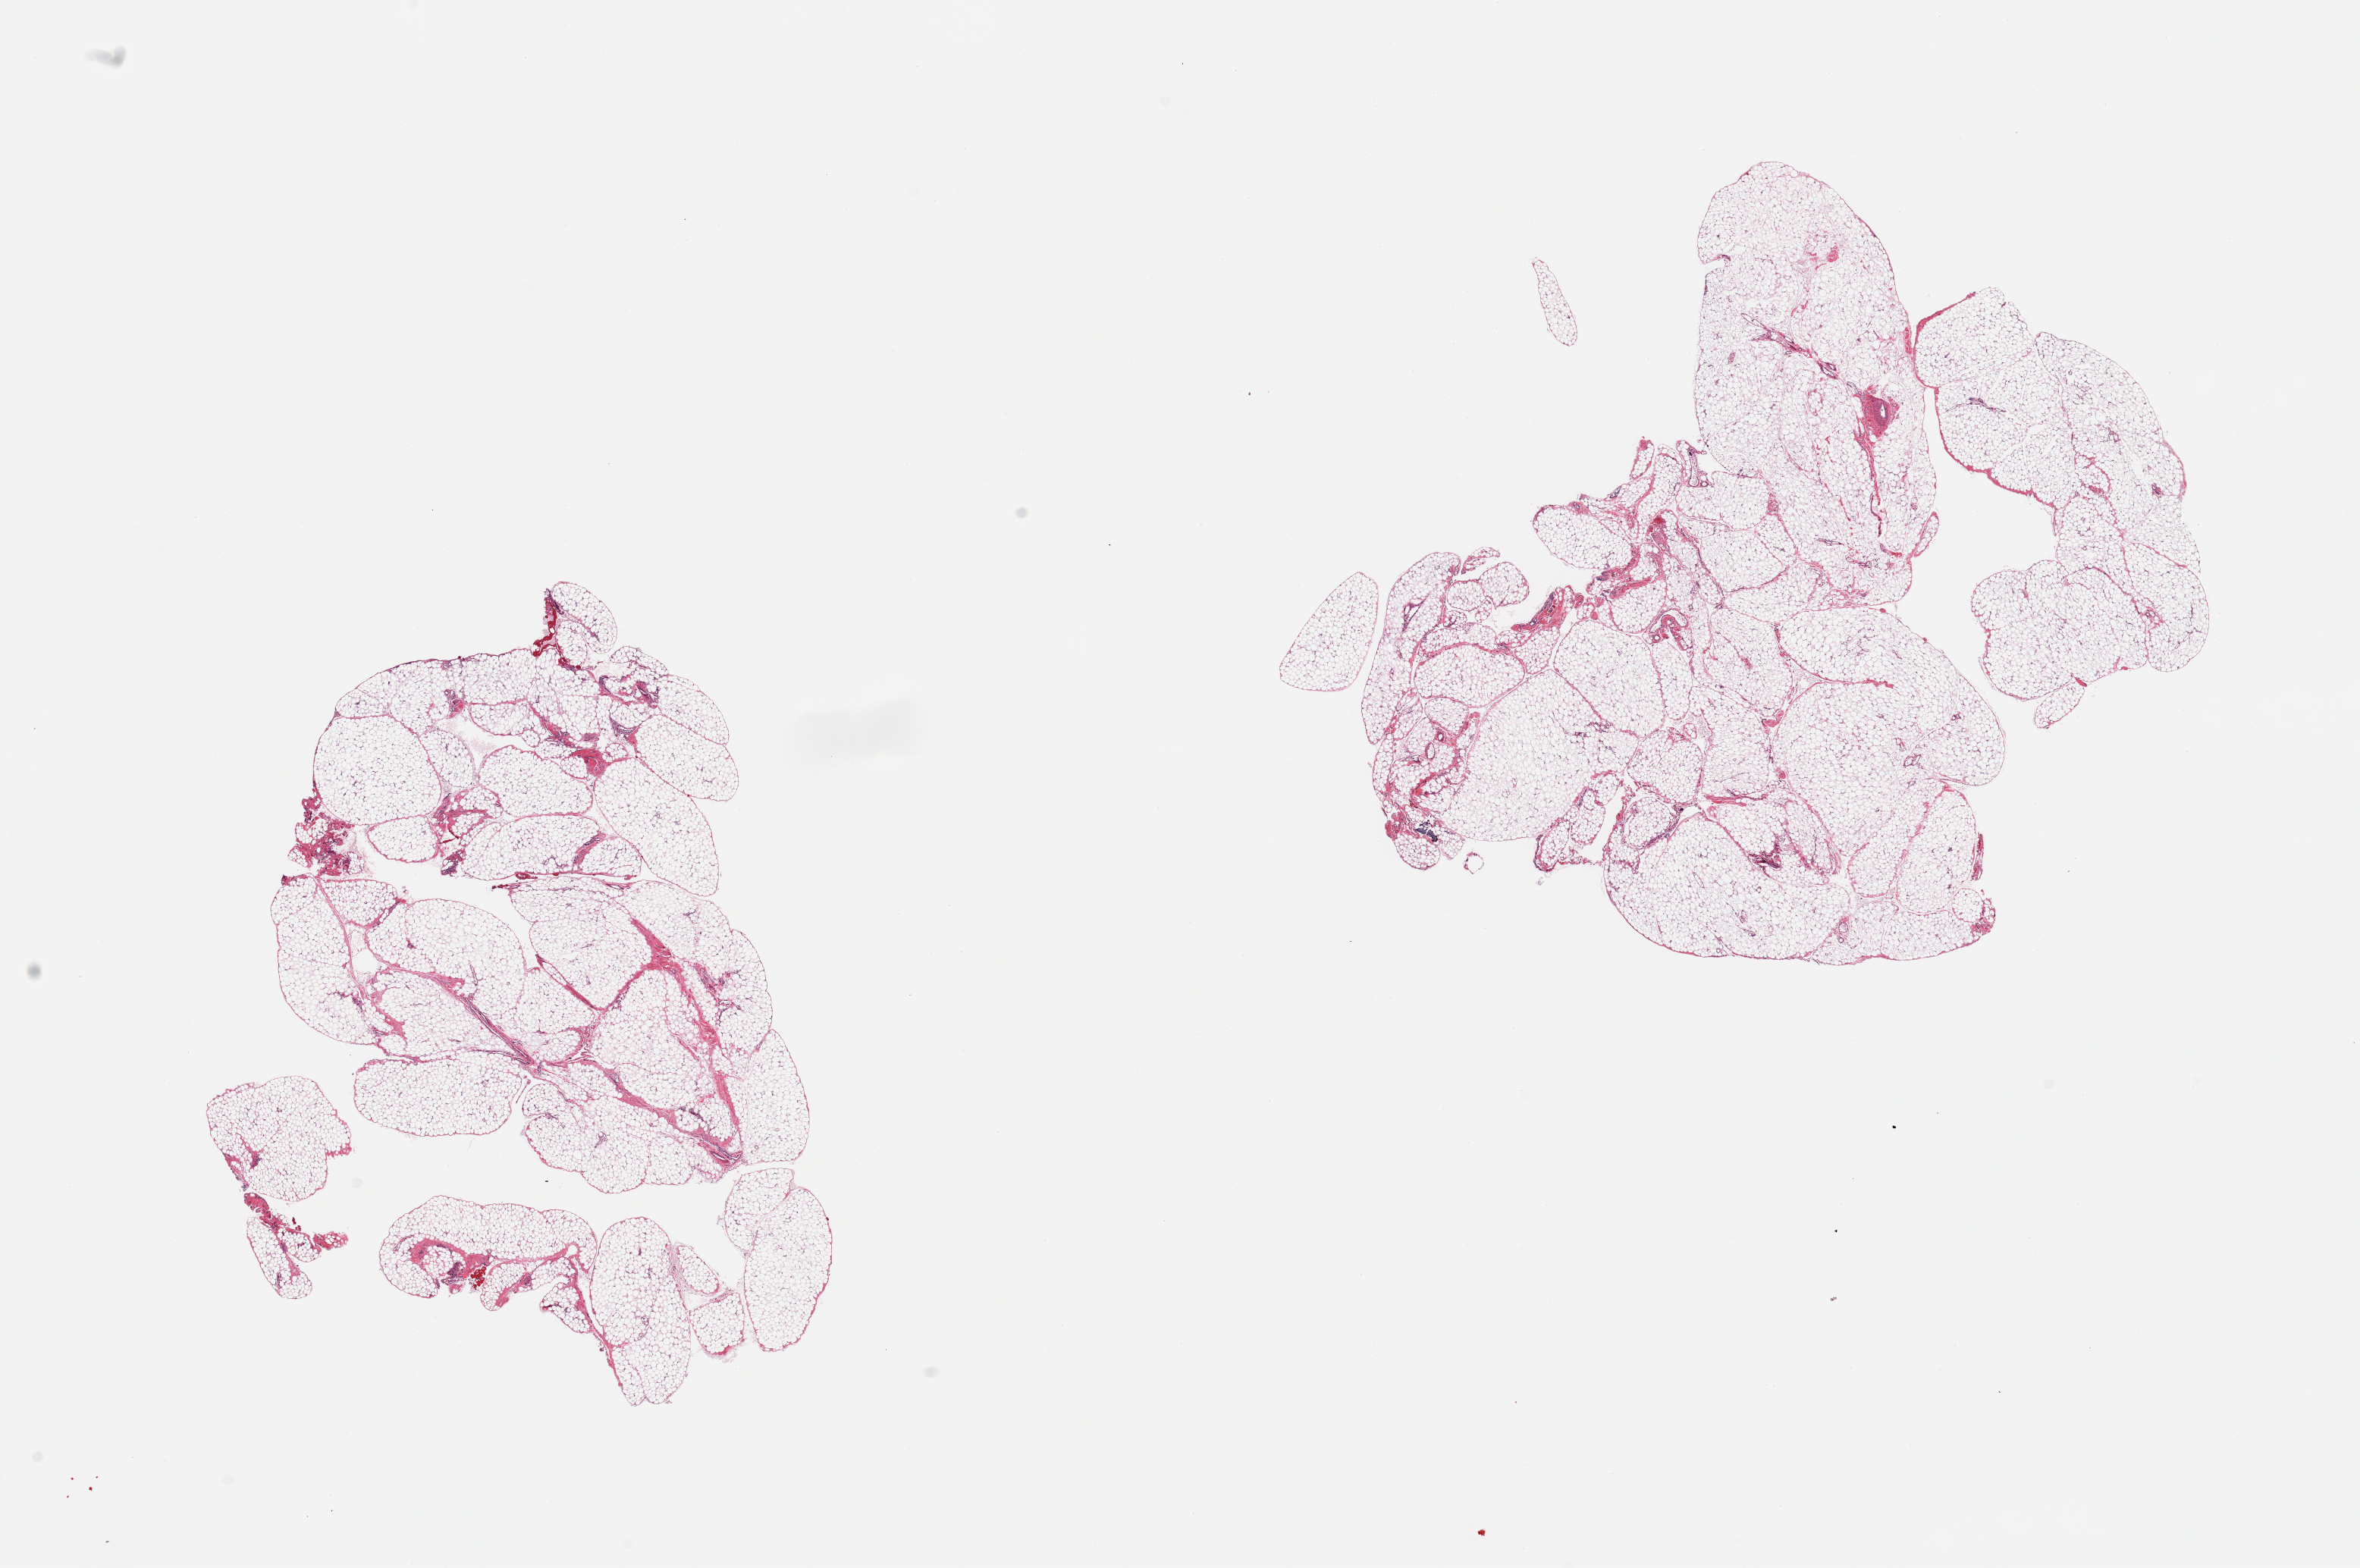
Hematoxylin and eosin (H&E) whole-slide image, whole scanned area (about 24.6 x 16.4 mm, slide scanned at 20x) shown as a low-resolution overview. PAXgene-fixed paraffin-embedded (PFPE) section. Section of omentum (target tissue). Tissue donor sample. Donor sex: male.
Review note (as recorded): 2 pieces.